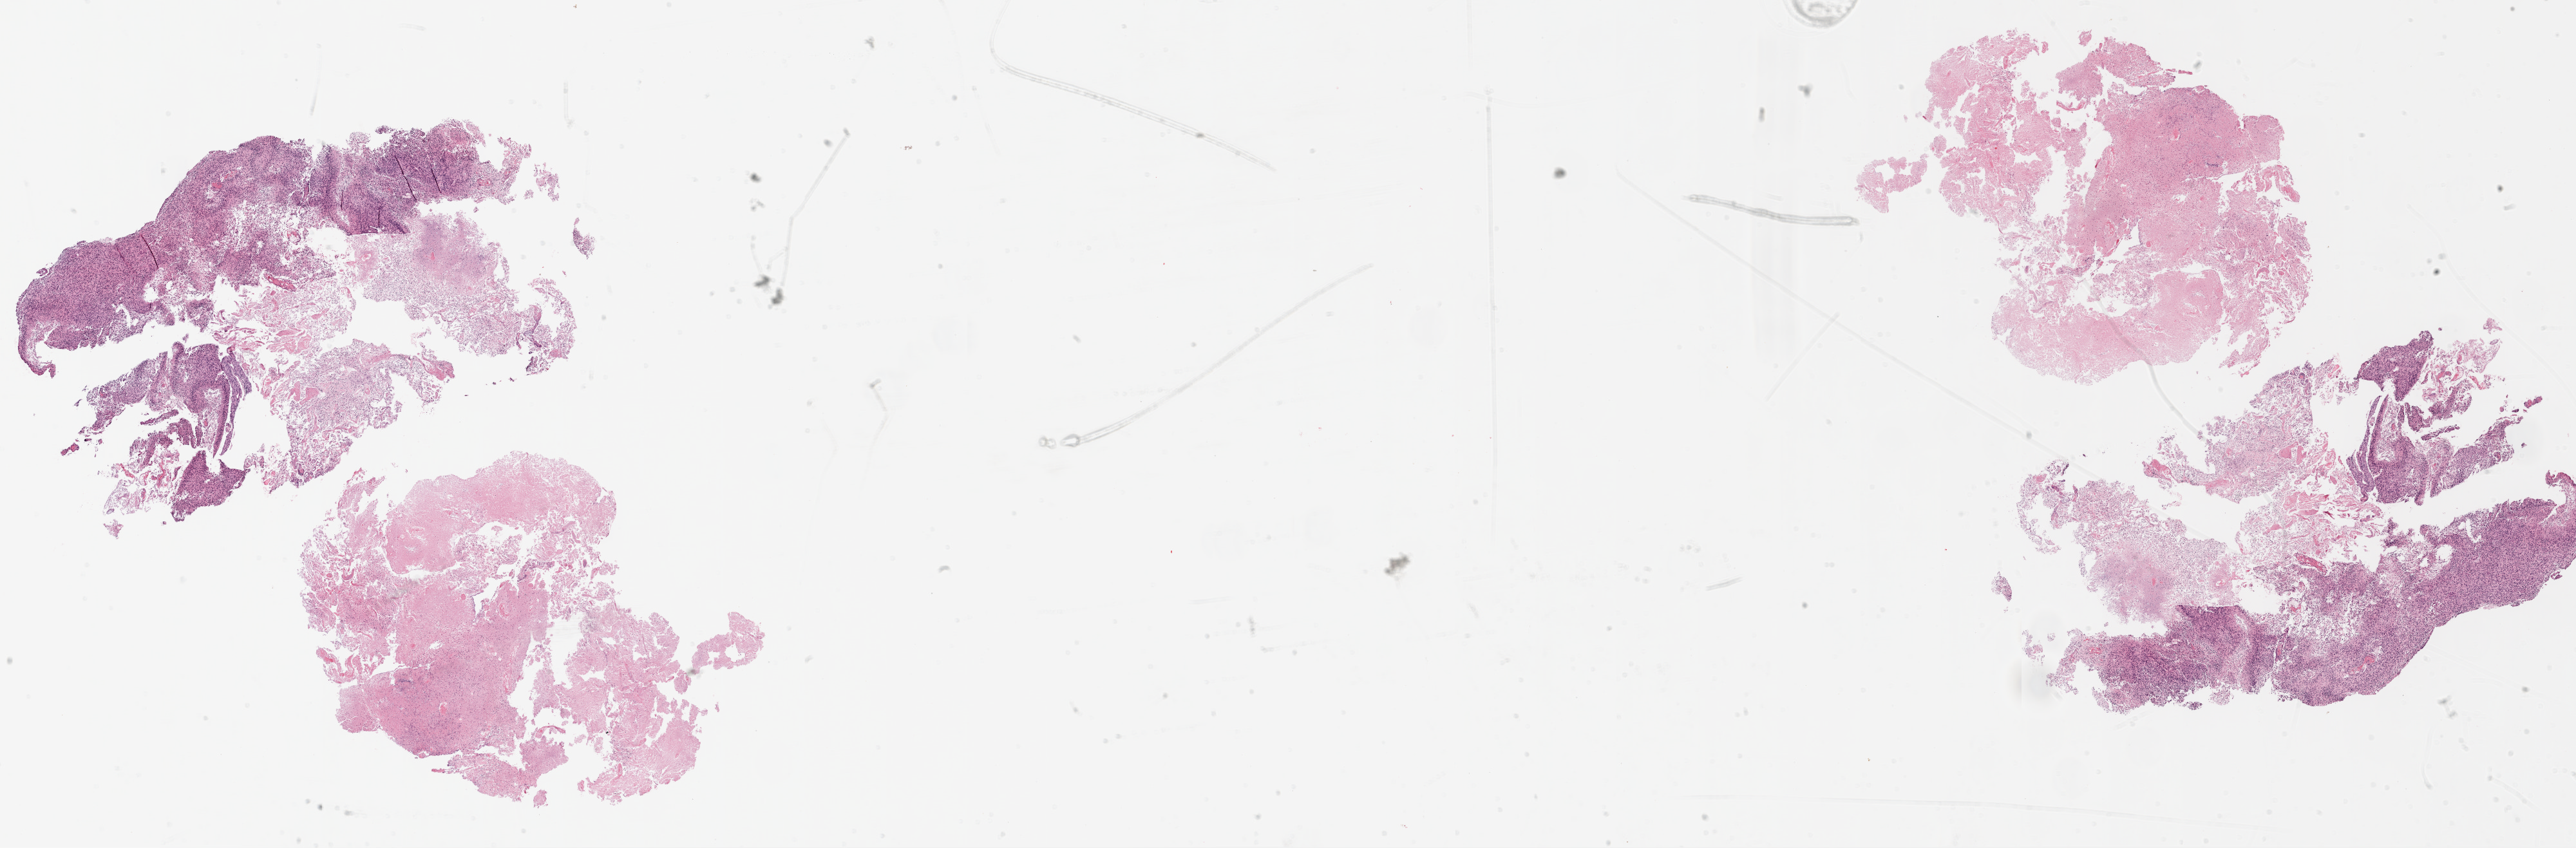
Digitized H&E-stained tissue section (whole slide), shown as a low-resolution overview of the whole scanned area (about 32.1 x 10.6 mm, slide scanned at 20x); formalin-fixed paraffin-embedded (FFPE) diagnostic section; brain, primary tumour sample. Male, age 60 years at initial diagnosis.
- diagnosis: Glioblastoma